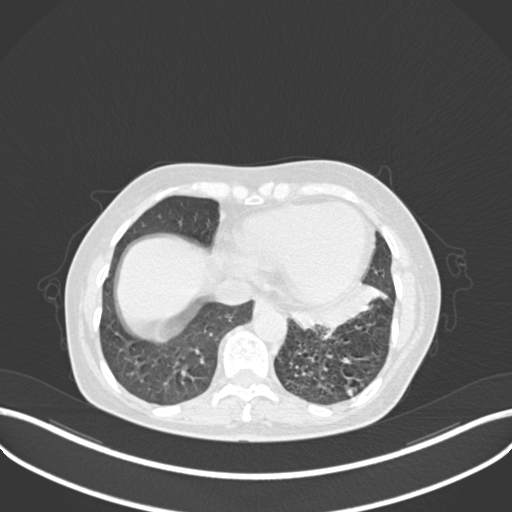
Chest CT, one axial slice; position 73 of 270 along the scan axis; 120 kVp; lung window (W 1500 / L -600 HU); 1 mm slice thickness; 512 × 512 image matrix. Patient: female, 63 years. From the clinical record (not read from this slice): clinical TNM (as recorded): T1b N0 M0; histopathological grade: G2-3.
Annotated regions visible in this slice (rectangle marked by the reading radiologist):
- lung tumour (recorded histology: adenocarcinoma): box from (x=294, y=278) to (x=388, y=336) px